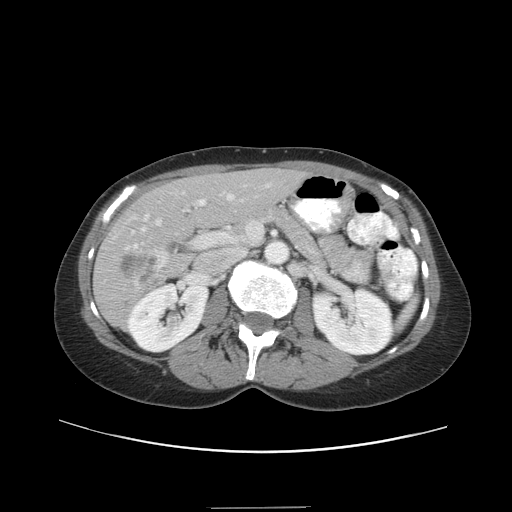
Contrast-enhanced abdominal CT, one axial slice. Position 18 of 38 along the scan axis. Reconstruction kernel STANDARD. 120 kVp. Intravenous contrast given. Soft-tissue window (W 400 / L 40 HU). 5 mm slice thickness. 512 × 512 image matrix, field of view 388 × 388 mm. Female patient, age 64 years. Case-level facts recorded for this patient, not image findings: diagnosis: colorectal cancer liver metastases, imaged before liver resection; multiple liver metastases: no; largest metastasis: 3.8 cm; disease in both lobes: yes.
Structures marked on this image (manually delineated by an expert):
- hepatic veins: bounding box <141,192,234,232> (left, top, right, bottom; pixels)
- liver: <96,170,304,327>
- planned liver remnant (the part of the liver to remain after resection): <141,170,304,233>
- portal vein (with intrahepatic branches): <125,199,206,270>
- liver metastasis: <121,255,157,283>